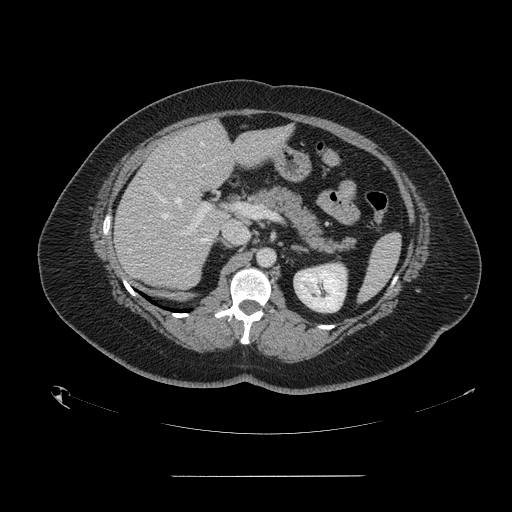
Contrast-enhanced abdominal CT, one axial slice; position 85 of 164 along the scan axis; 120 kVp; intravenous contrast given; soft-tissue window (W 400 / L 40 HU); 2.5 mm slice thickness; 512 × 512 image matrix, field of view 495 × 495 mm. Female patient, age 52 years. Case-level facts recorded for this patient, not image findings: diagnosis: colorectal cancer liver metastases, imaged before liver resection; multiple liver metastases: yes; largest metastasis: 3.5 cm; disease in both lobes: no.
Annotated regions visible in this slice (outlined manually by an expert reader):
- hepatic veins: bounding box <147,141,203,218> (left, top, right, bottom; pixels)
- liver: <114,121,288,289>
- planned liver remnant (the part of the liver to remain after resection): <177,121,288,189>
- portal vein (with intrahepatic branches): <169,184,210,234>